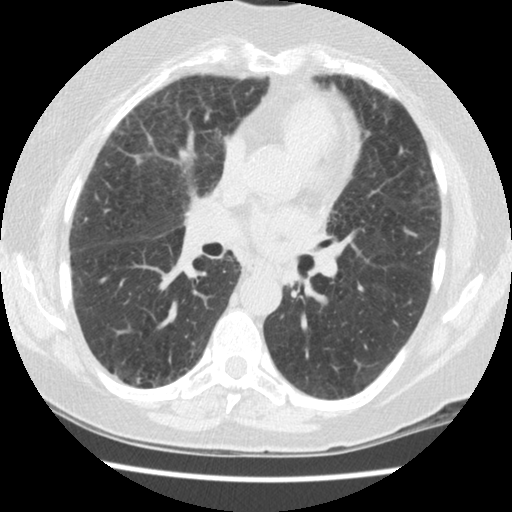
Axial slice from a low-dose chest CT screening exam; second screening round (one year after baseline); lung window (W 1500 / L -600 HU); 2.5 mm slice thickness. Female participant, aged 60 years at enrolment. Former smoker at enrolment.
Expert-annotated lung lesion, box from (x=269, y=256) to (x=316, y=301) px. Reader record for this screening exam (exam-level; its link to the box is not recorded): non-calcified nodule or mass ≥4 mm, left lower lobe, 5 × 4 mm, smooth margins, soft tissue attenuation, pre-existing on the prior screen: yes; interval growth: no.